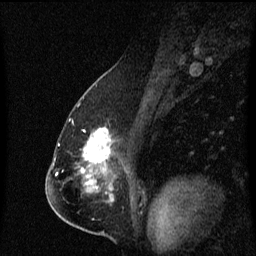
Breast MRI (dynamic contrast-enhanced), one sagittal slice. Slice 38 of 60 in the series (ordered by position). Dynamic contrast-enhanced series, image 2 of 3 at this slice position (ordered by acquisition). 1.5 T. TE 4.2 ms, TR 8.4 ms. 2 mm slice thickness. 256 × 256 image matrix, field of view 200 × 200 mm. Female patient, age 57 years. From the clinical record (not read from this slice): setting: breast cancer imaged before/during neoadjuvant chemotherapy; receptor status: HR-positive, HER2-negative.
Structures marked on this image (semi-automatically segmented with operator editing):
- analysis volume of interest (the breast-tissue region the enhancement analysis was run in; not a lesion): bounding box [x1, y1, x2, y2] px = [75, 128, 127, 177]
- tumour enhancement mask (voxels above the 70 % enhancement threshold inside the analysis volume of interest): [80, 128, 111, 173]